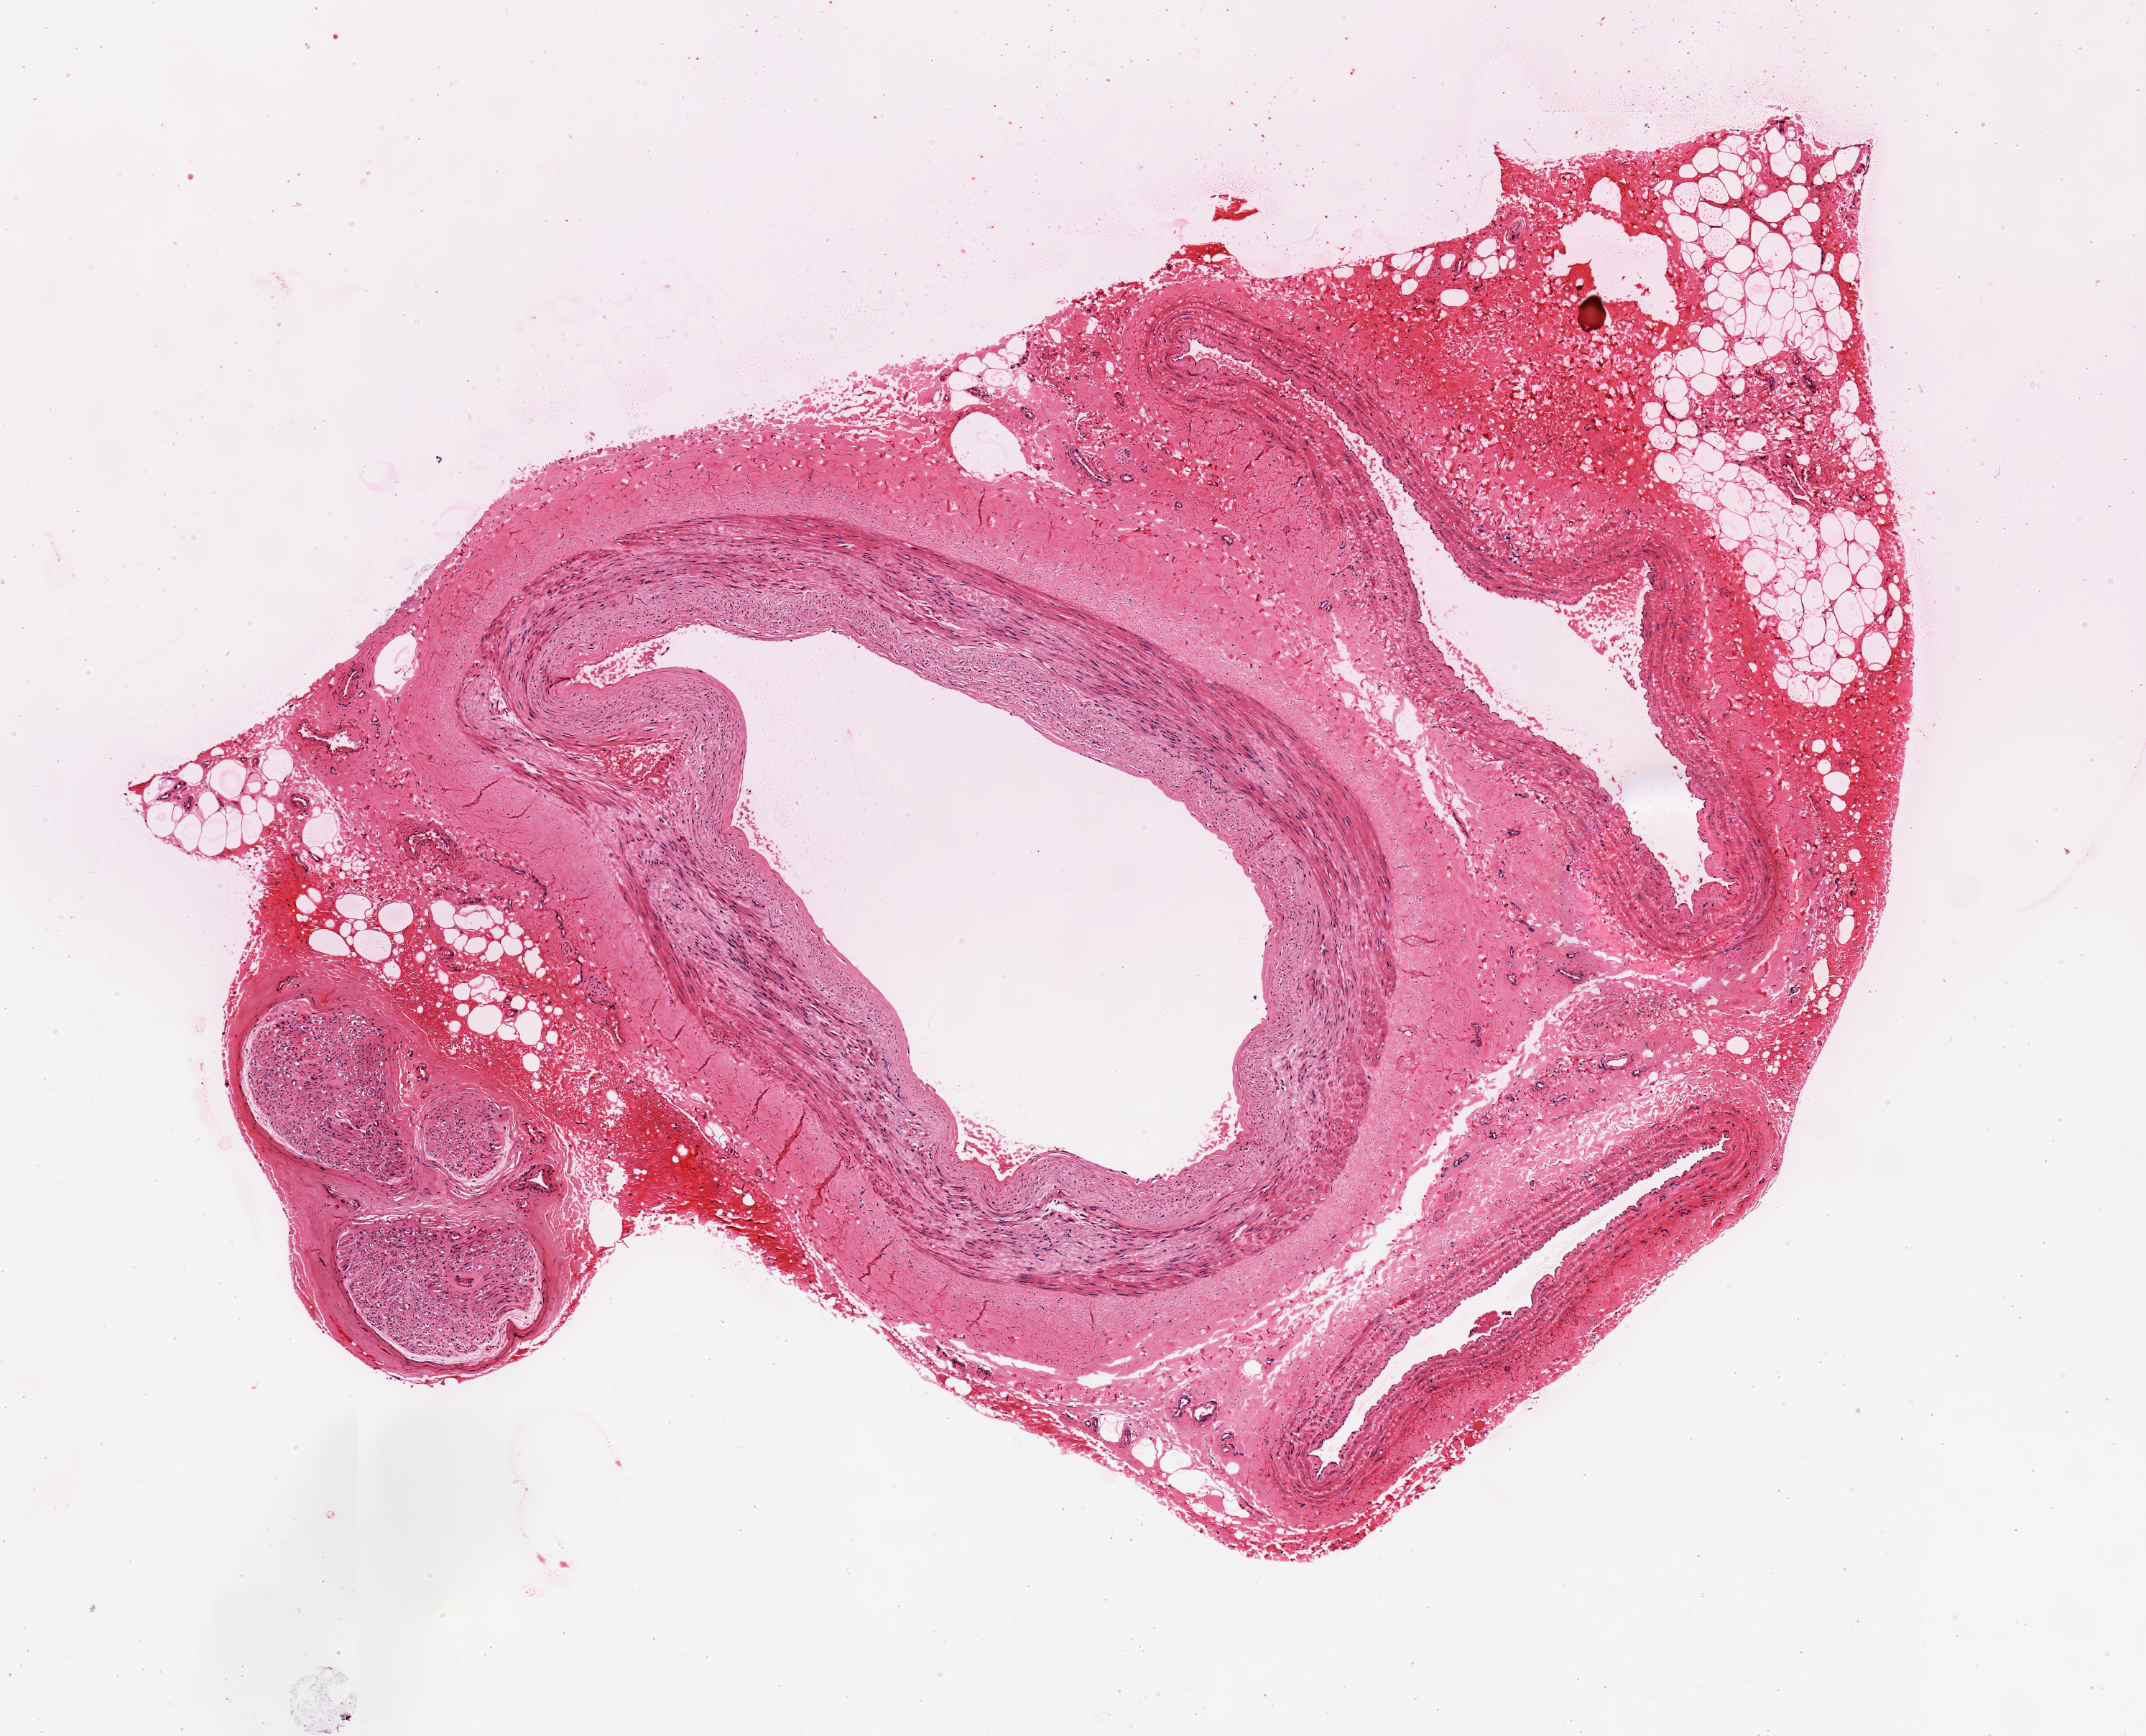
Hematoxylin and eosin (H&E) whole-slide image, brightfield — a low-resolution overview of the entire scanned area, about 5.9 x 4.8 mm (acquisition: 20x scan); PAXgene-fixed, paraffin-embedded tissue; section of tibial artery (target tissue); tissue donor sample. Female donor.
* pathologist's review note for this sample: artery is ~50% of specimen; remainder is fat and veins